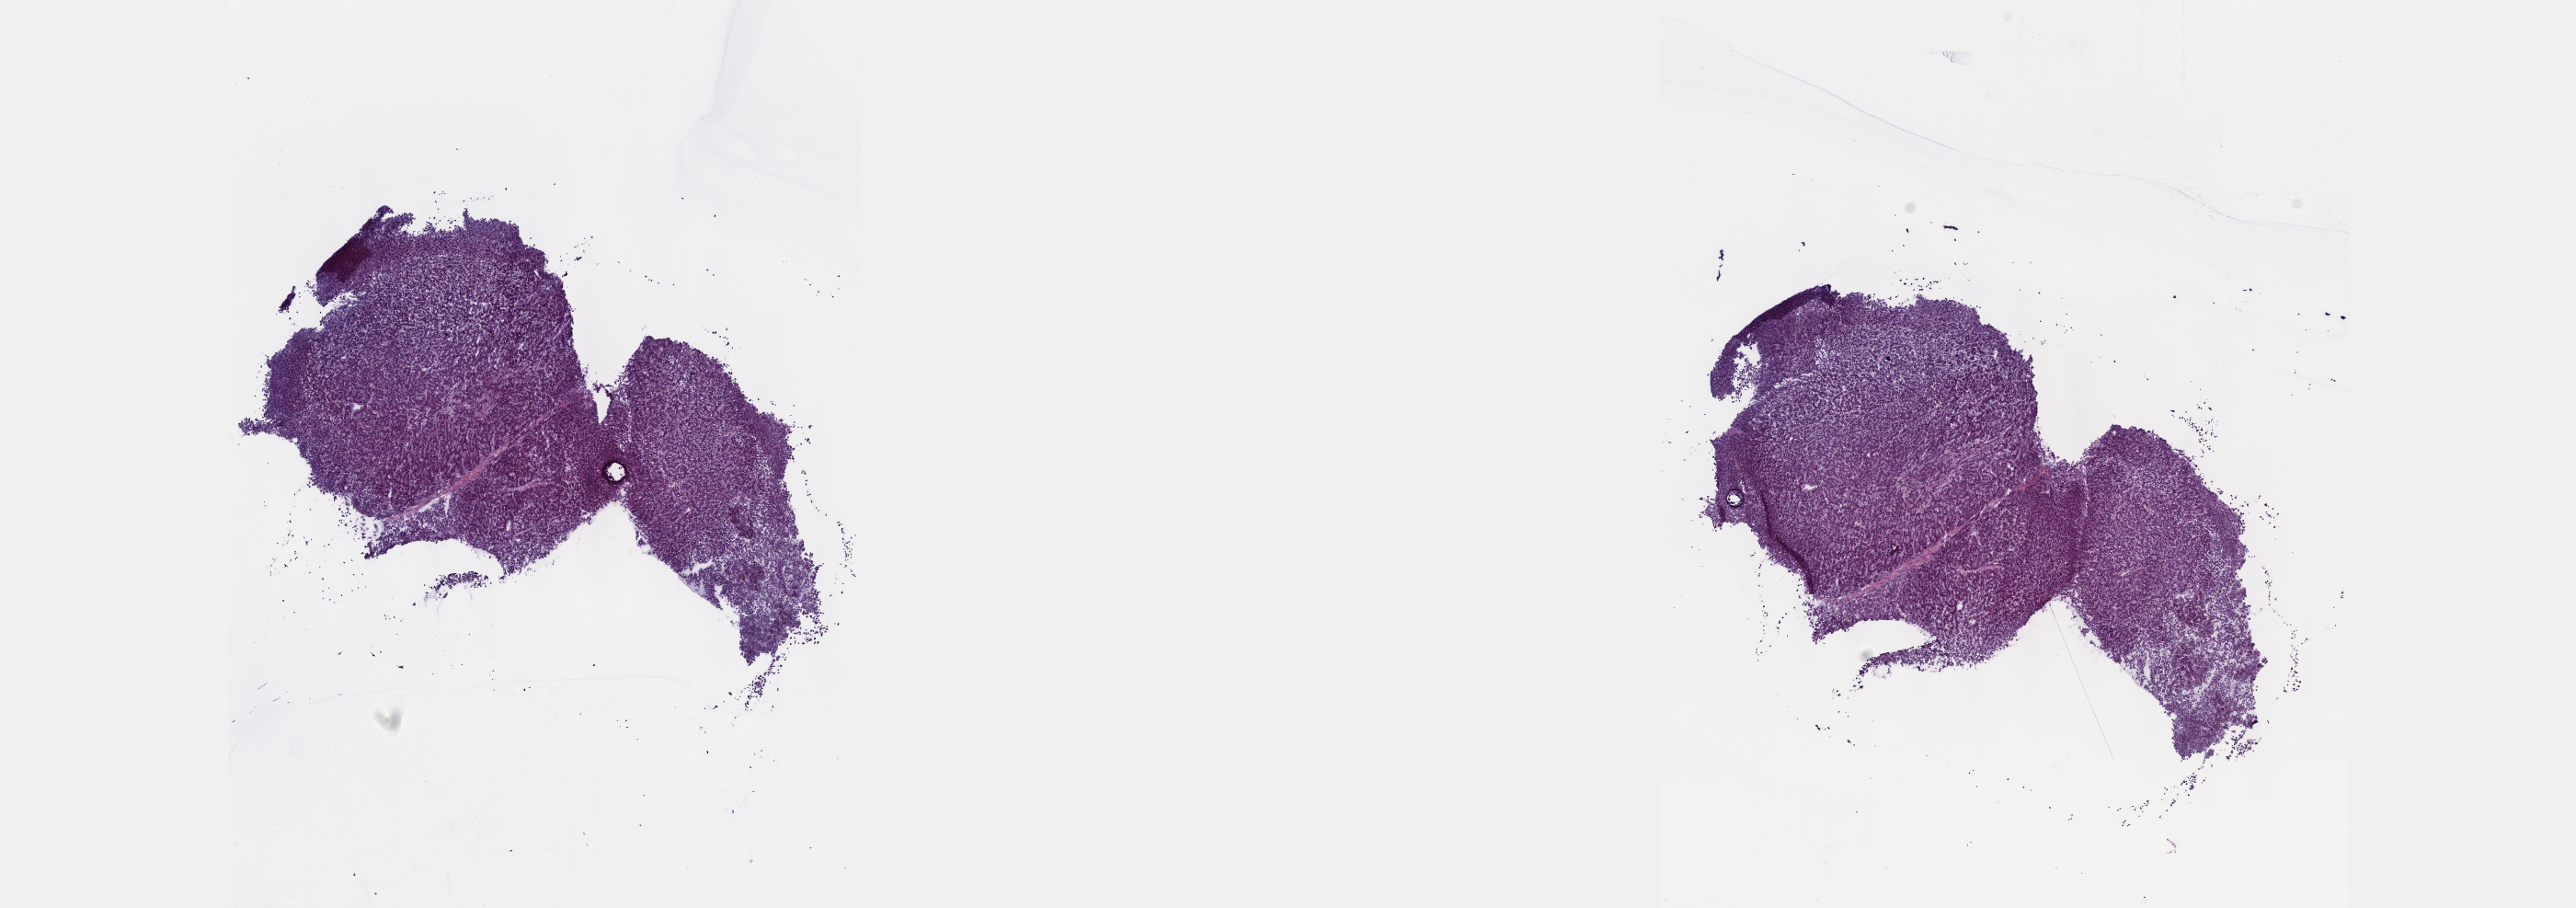
H&E whole-slide image — whole scanned area (about 22.6 x 8.0 mm, from a 40x scan) shown as a low-resolution overview; frozen section from the top of the tissue portion; sample: primary tumour, liver. Patient: male, age at initial diagnosis 59 years. Histologic grade: G1 (well differentiated). Slide review estimates, as recorded: tumour cells 100%, tumour nuclei 75%, normal cells 0%, stromal cells 0%, necrosis 0%. Infiltration values recorded for this section: lymphocyte infiltration 0%, monocyte infiltration 0%, neutrophil infiltration 0%.
Pathologic diagnosis: Hepatocellular carcinoma, NOS.